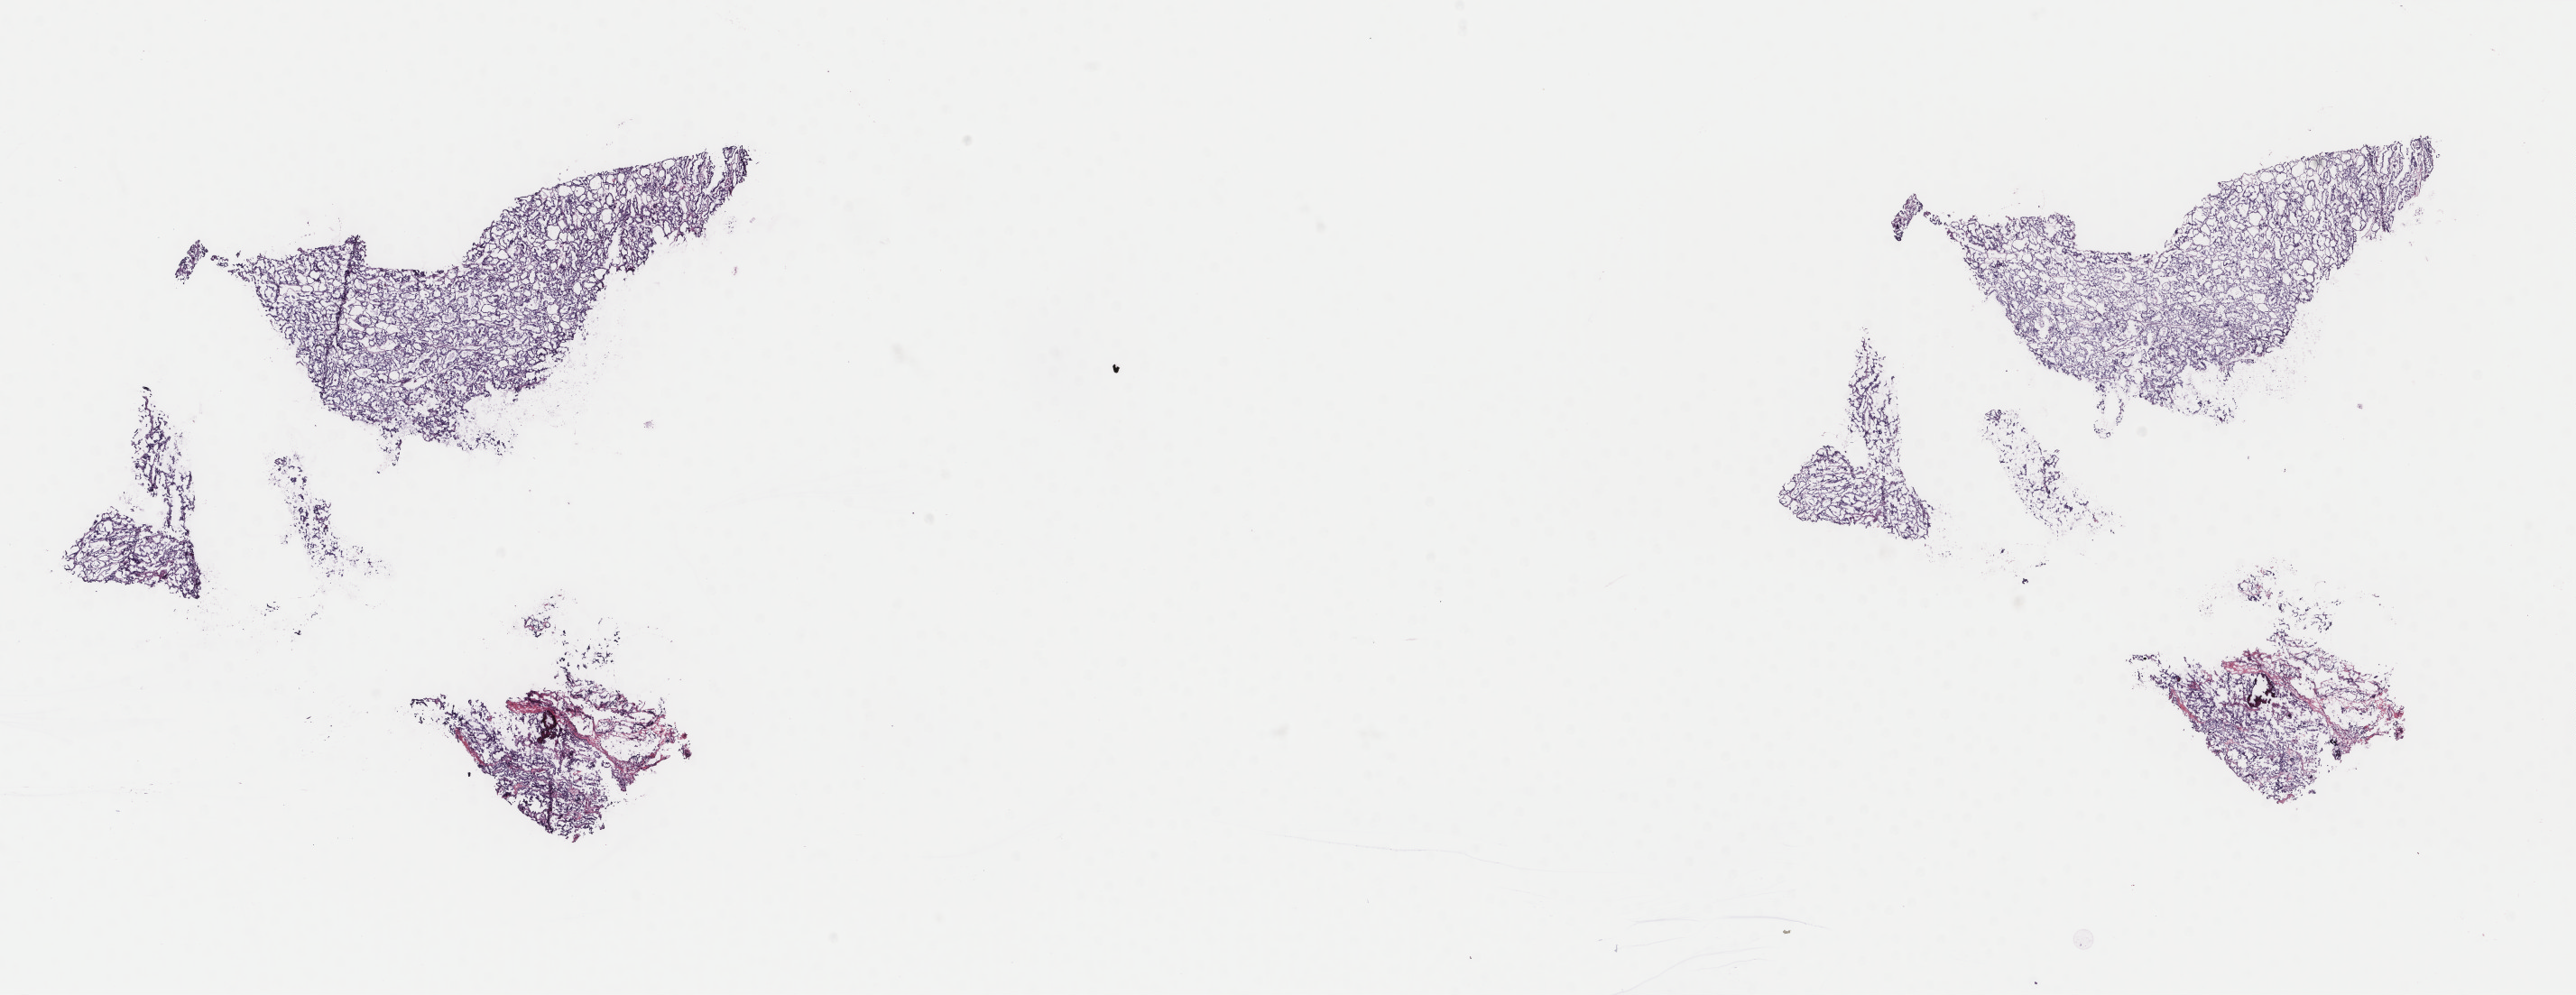
H&E-stained whole-slide image, whole scanned area (about 22.7 x 8.8 mm) shown as a low-resolution overview. Frozen section from the top of the tissue portion. Sample: primary tumour, thyroid. Patient: female, age at initial diagnosis 24 years. Slide review estimates, as recorded: tumour cells 75%, tumour nuclei 95%, normal cells 0%, stromal cells 25%, necrosis 0%. Inflammatory infiltration, as recorded: lymphocyte infiltration 1%, monocyte infiltration 0%, neutrophil infiltration 0%.
AJCC pathologic stage: I (7th edition). Lymph nodes positive (case pathology): 7 of 20 examined. Pathologic diagnosis: Papillary carcinoma, follicular variant (thyroid gland).